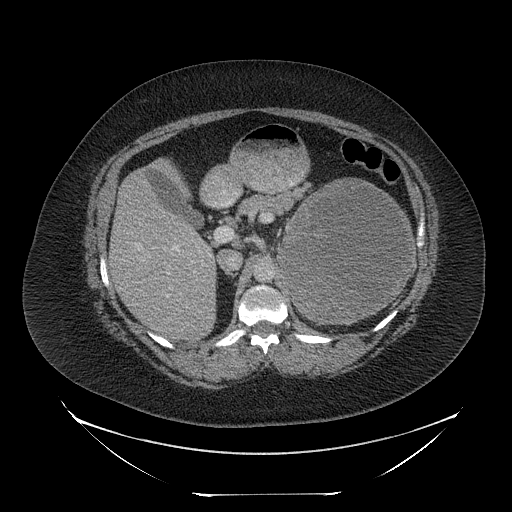
Contrast-enhanced abdominal CT, one axial slice; slice 145 of 205 in the series (ordered by position); 120 kVp; intravenous contrast given; soft-tissue window (W 400 / L 40 HU); 2.5 mm slice thickness; 512 × 512 image matrix, field of view 500 × 500 mm. Patient: female, 53 years. From the clinical record (not read from this slice): diagnosis: adrenocortical carcinoma; tumour side: left adrenal; tumour size at pathology: 17 cm; Ki-67 index: 20 %; stage (as recorded): 3.
Annotated regions visible in this slice (semi-automatic segmentation, software-assisted and operator-edited):
- mass: bounding box (x1, y1, x2, y2) in pixels: (281, 181, 412, 320)